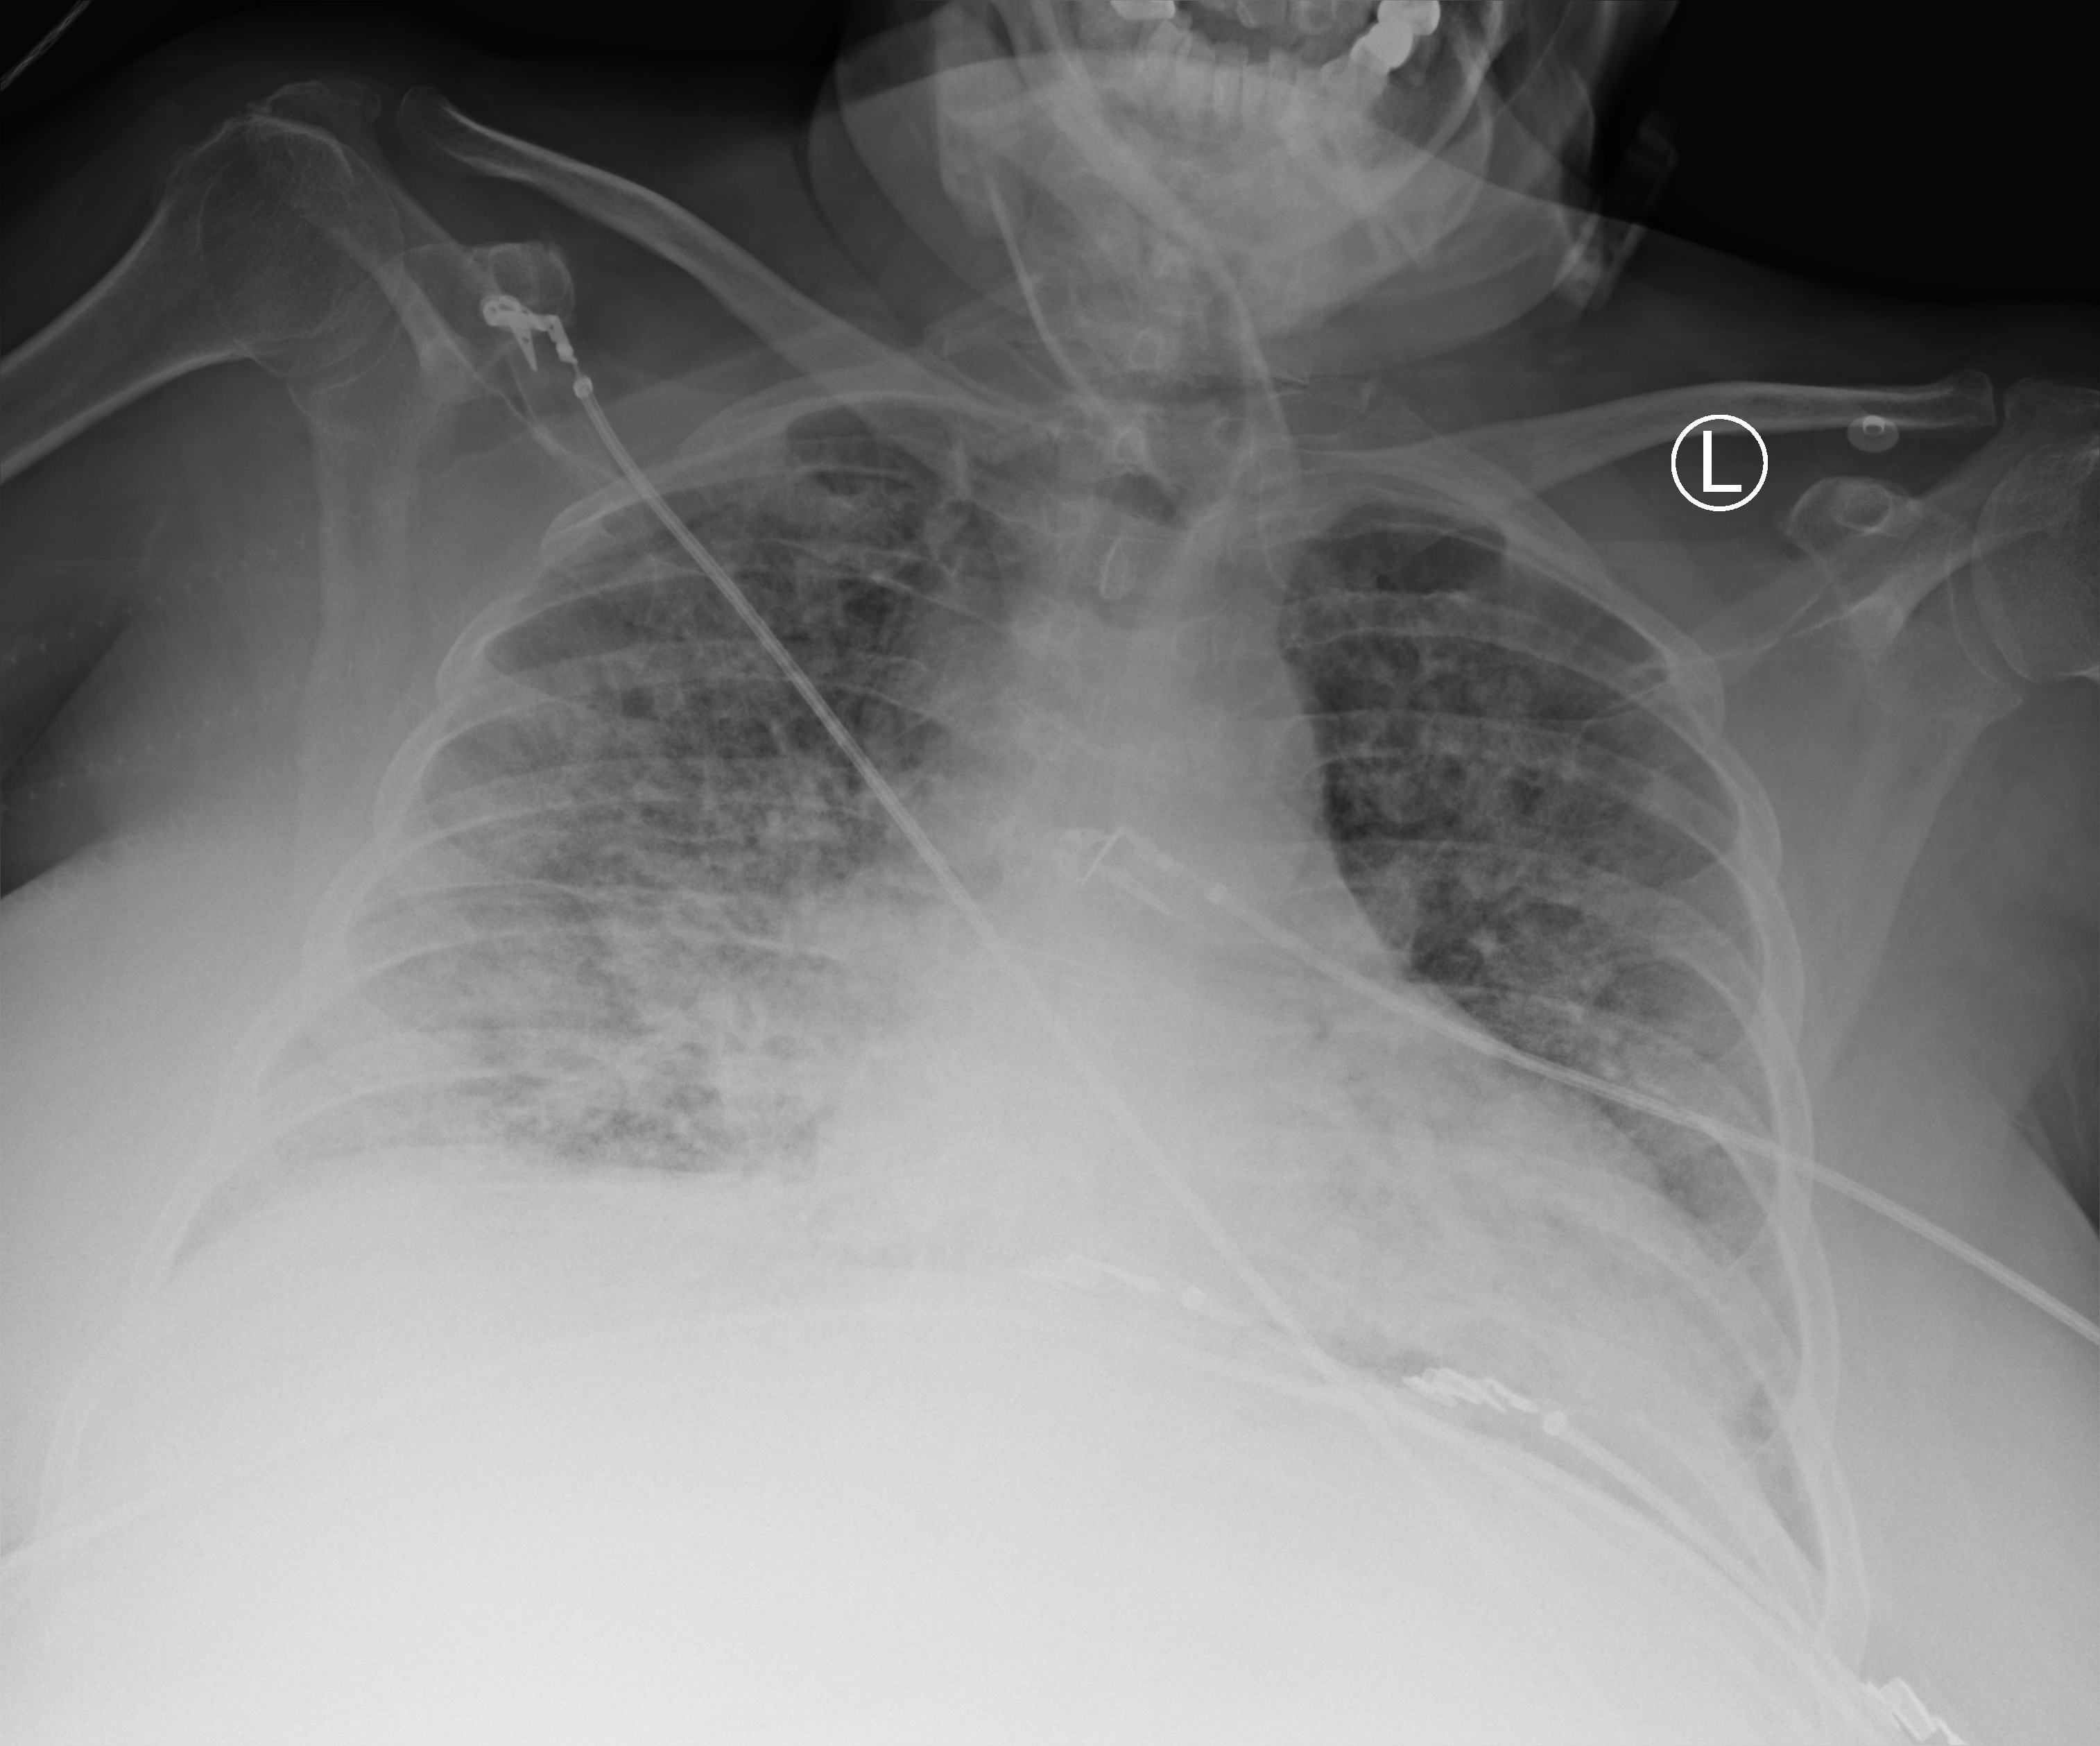
Chest X-ray (portable). Patient hospitalised with COVID-19; female, aged 60–74 years.
Admission-level facts for this patient (not findings on this image; timing relative to this image not recorded):
- length of hospital stay: 18 days
- chronic kidney disease (admission record): no
- admitted to intensive care during this hospital stay: yes